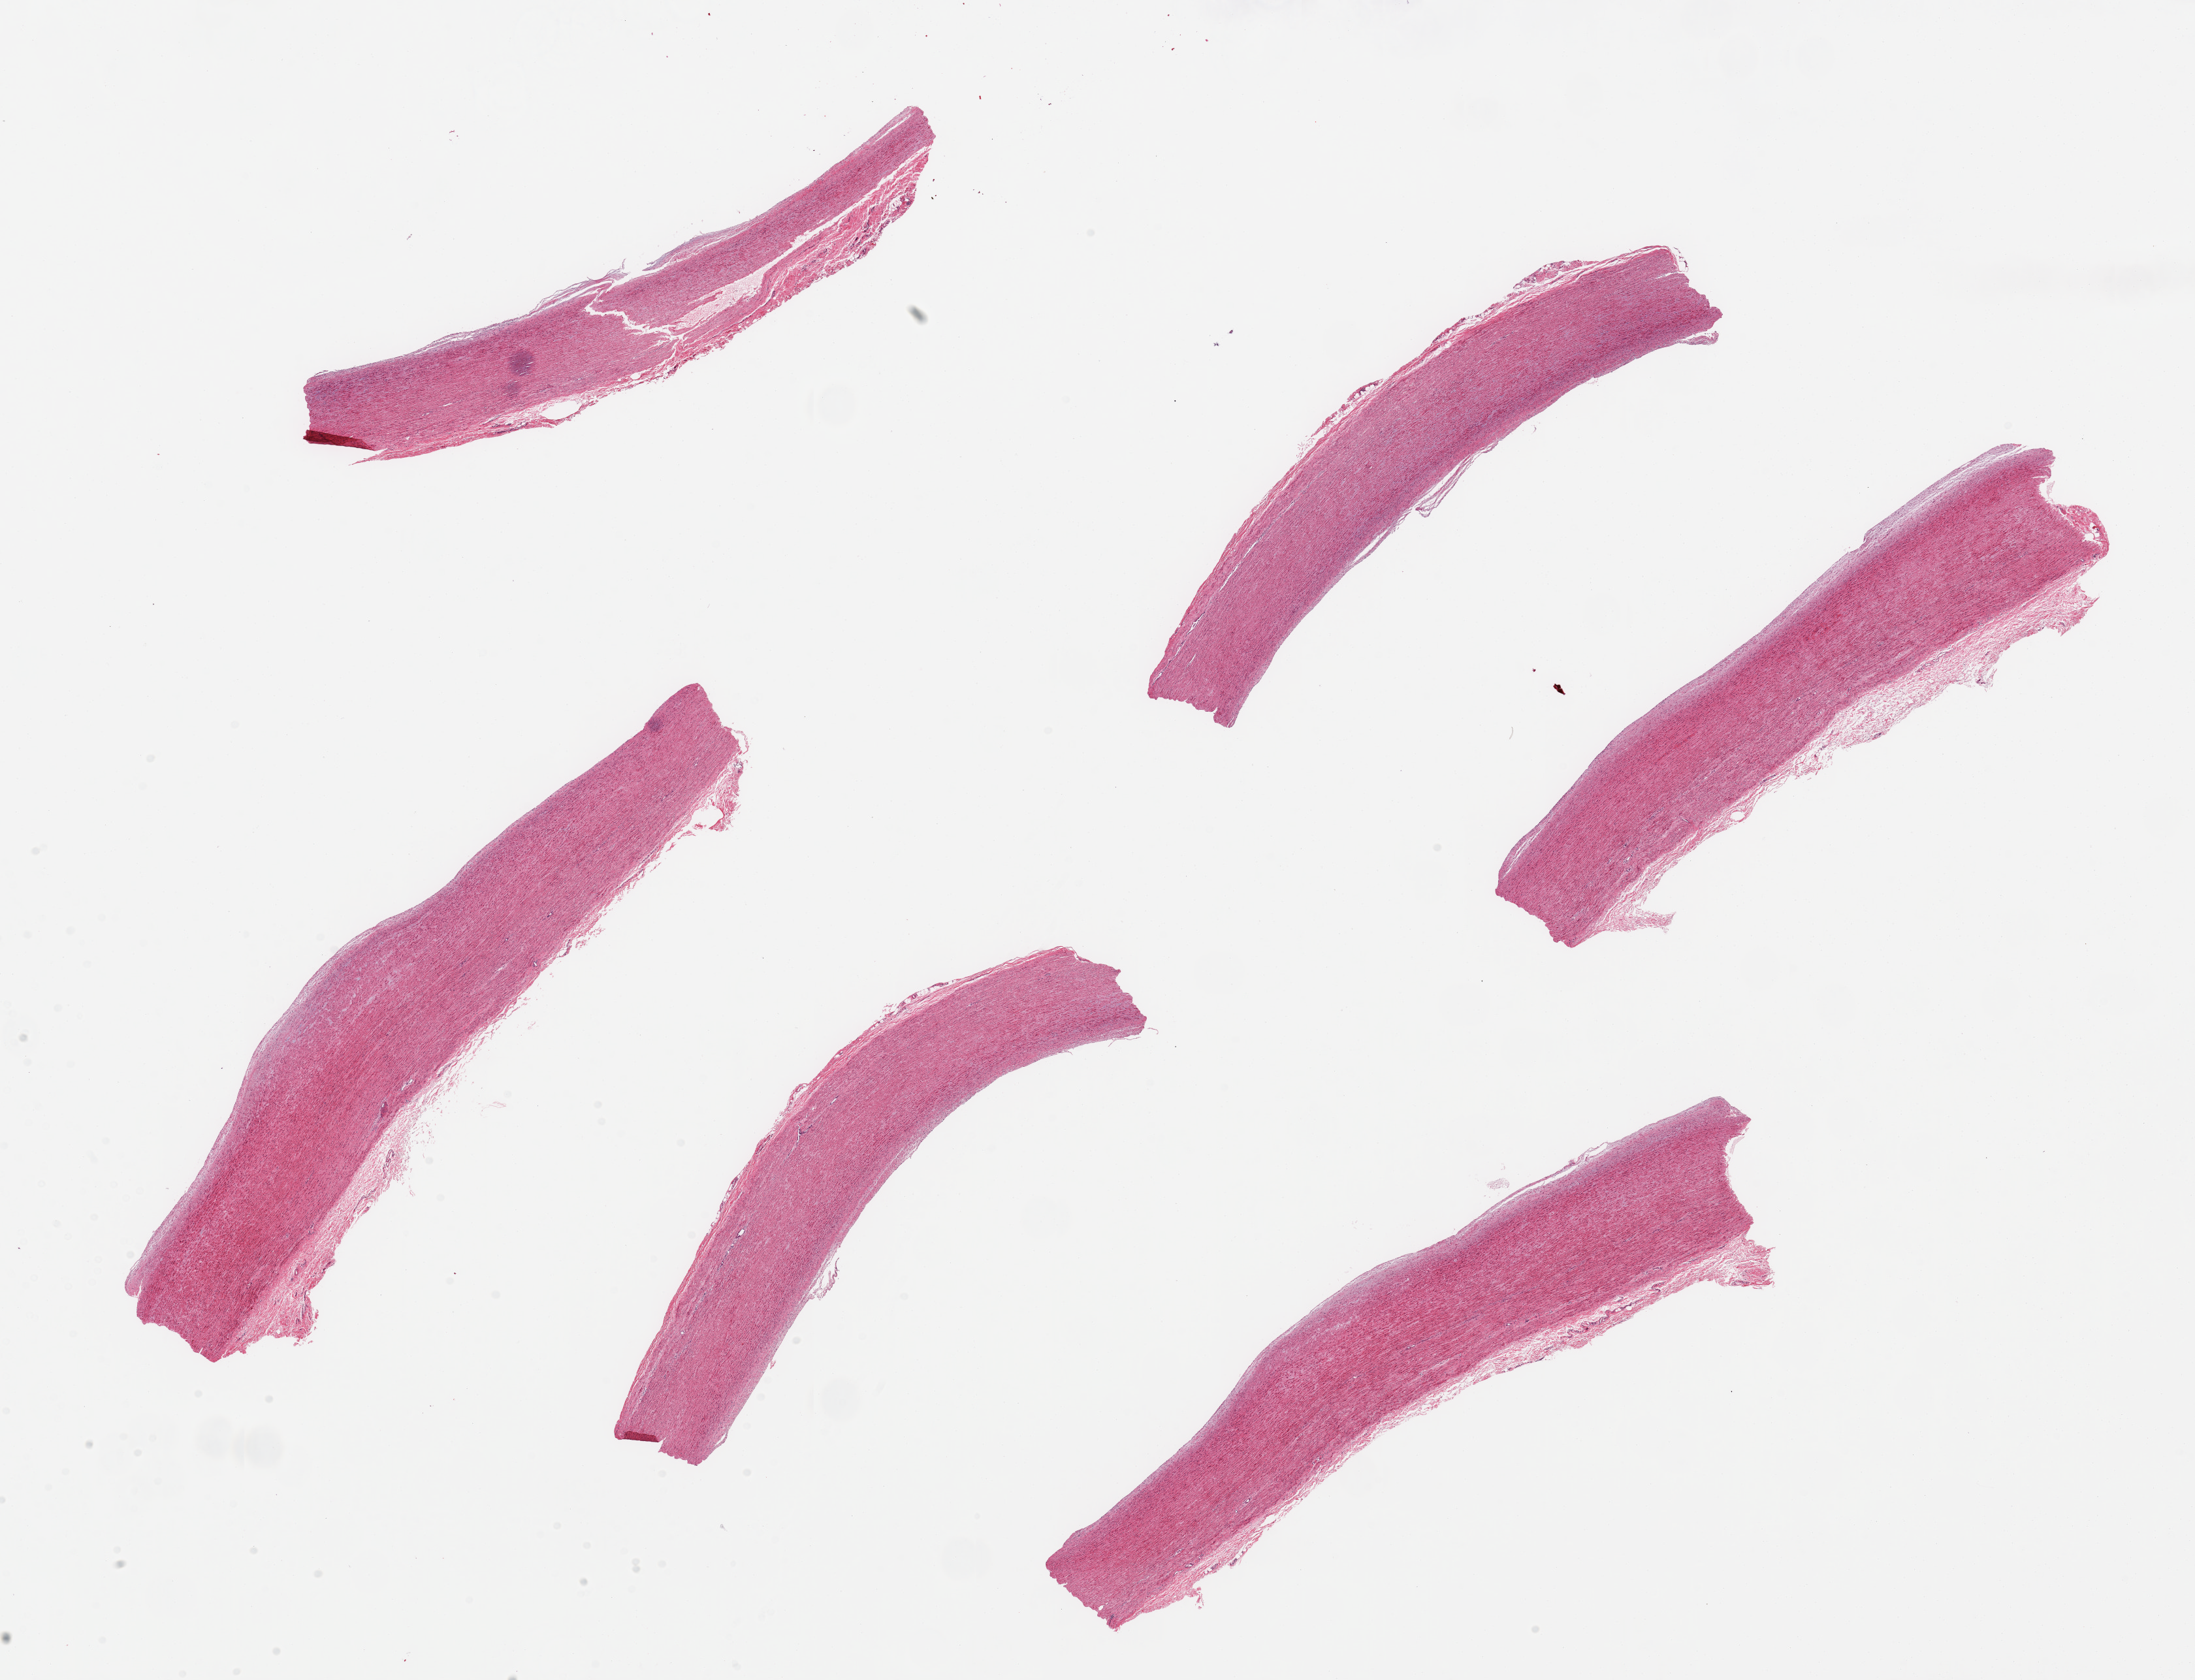
Digitized hematoxylin and eosin (H&E)-stained section, a low-resolution overview of the entire scanned area, about 26.6 x 20.3 mm (slide scanned at 20x). PAXgene-fixed paraffin-embedded (PFPE) section. Target tissue: aorta. Donor tissue sample. Male donor.
* reviewer comment on this tissue sample: 6 pieces; mild plaque